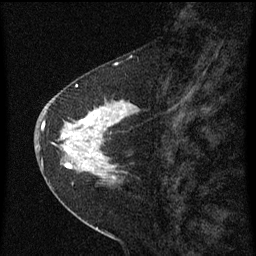
Breast MRI (dynamic contrast-enhanced), one sagittal slice. Position 26 of 60 along the scan axis. Dynamic contrast-enhanced series, image 2 of 3 at this slice position (ordered by acquisition). 1.5 T. TE 4.2 ms, TR 8 ms. 2 mm slice thickness. 256 × 256 image matrix. Female patient, age 47 years.
Structures marked on this image (semi-automatically segmented with operator editing):
- analysis volume of interest (the breast-tissue region the enhancement analysis was run in; not a lesion): bounding box [x1, y1, x2, y2] px = [44, 84, 139, 199]
- tumour enhancement mask (voxels above the 70 % enhancement threshold inside the analysis volume of interest): [44, 84, 139, 179]